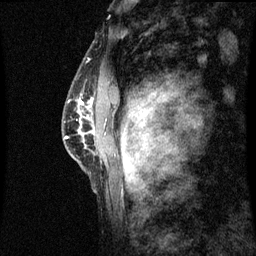
Breast MRI (dynamic contrast-enhanced), one sagittal slice; slice 45 of 60 in the series (ordered by position); dynamic contrast-enhanced series, image 2 of 3 at this slice position (ordered by acquisition); 1.5 T; TE 4.2 ms, TR 8.9 ms; 2 mm slice thickness; 256 × 256 image matrix, field of view 200 × 200 mm. Patient: female, 50 years. From the clinical record (not read from this slice): setting: breast cancer imaged before/during neoadjuvant chemotherapy; receptor status: triple-negative.
Structures marked on this image (semi-automatic segmentation, software-assisted and operator-edited):
- analysis volume of interest (the breast-tissue region the enhancement analysis was run in; not a lesion): bounding box [x1, y1, x2, y2] px = [68, 80, 97, 169]
- tumour enhancement mask (voxels above the 70 % enhancement threshold inside the analysis volume of interest): [68, 102, 95, 139]